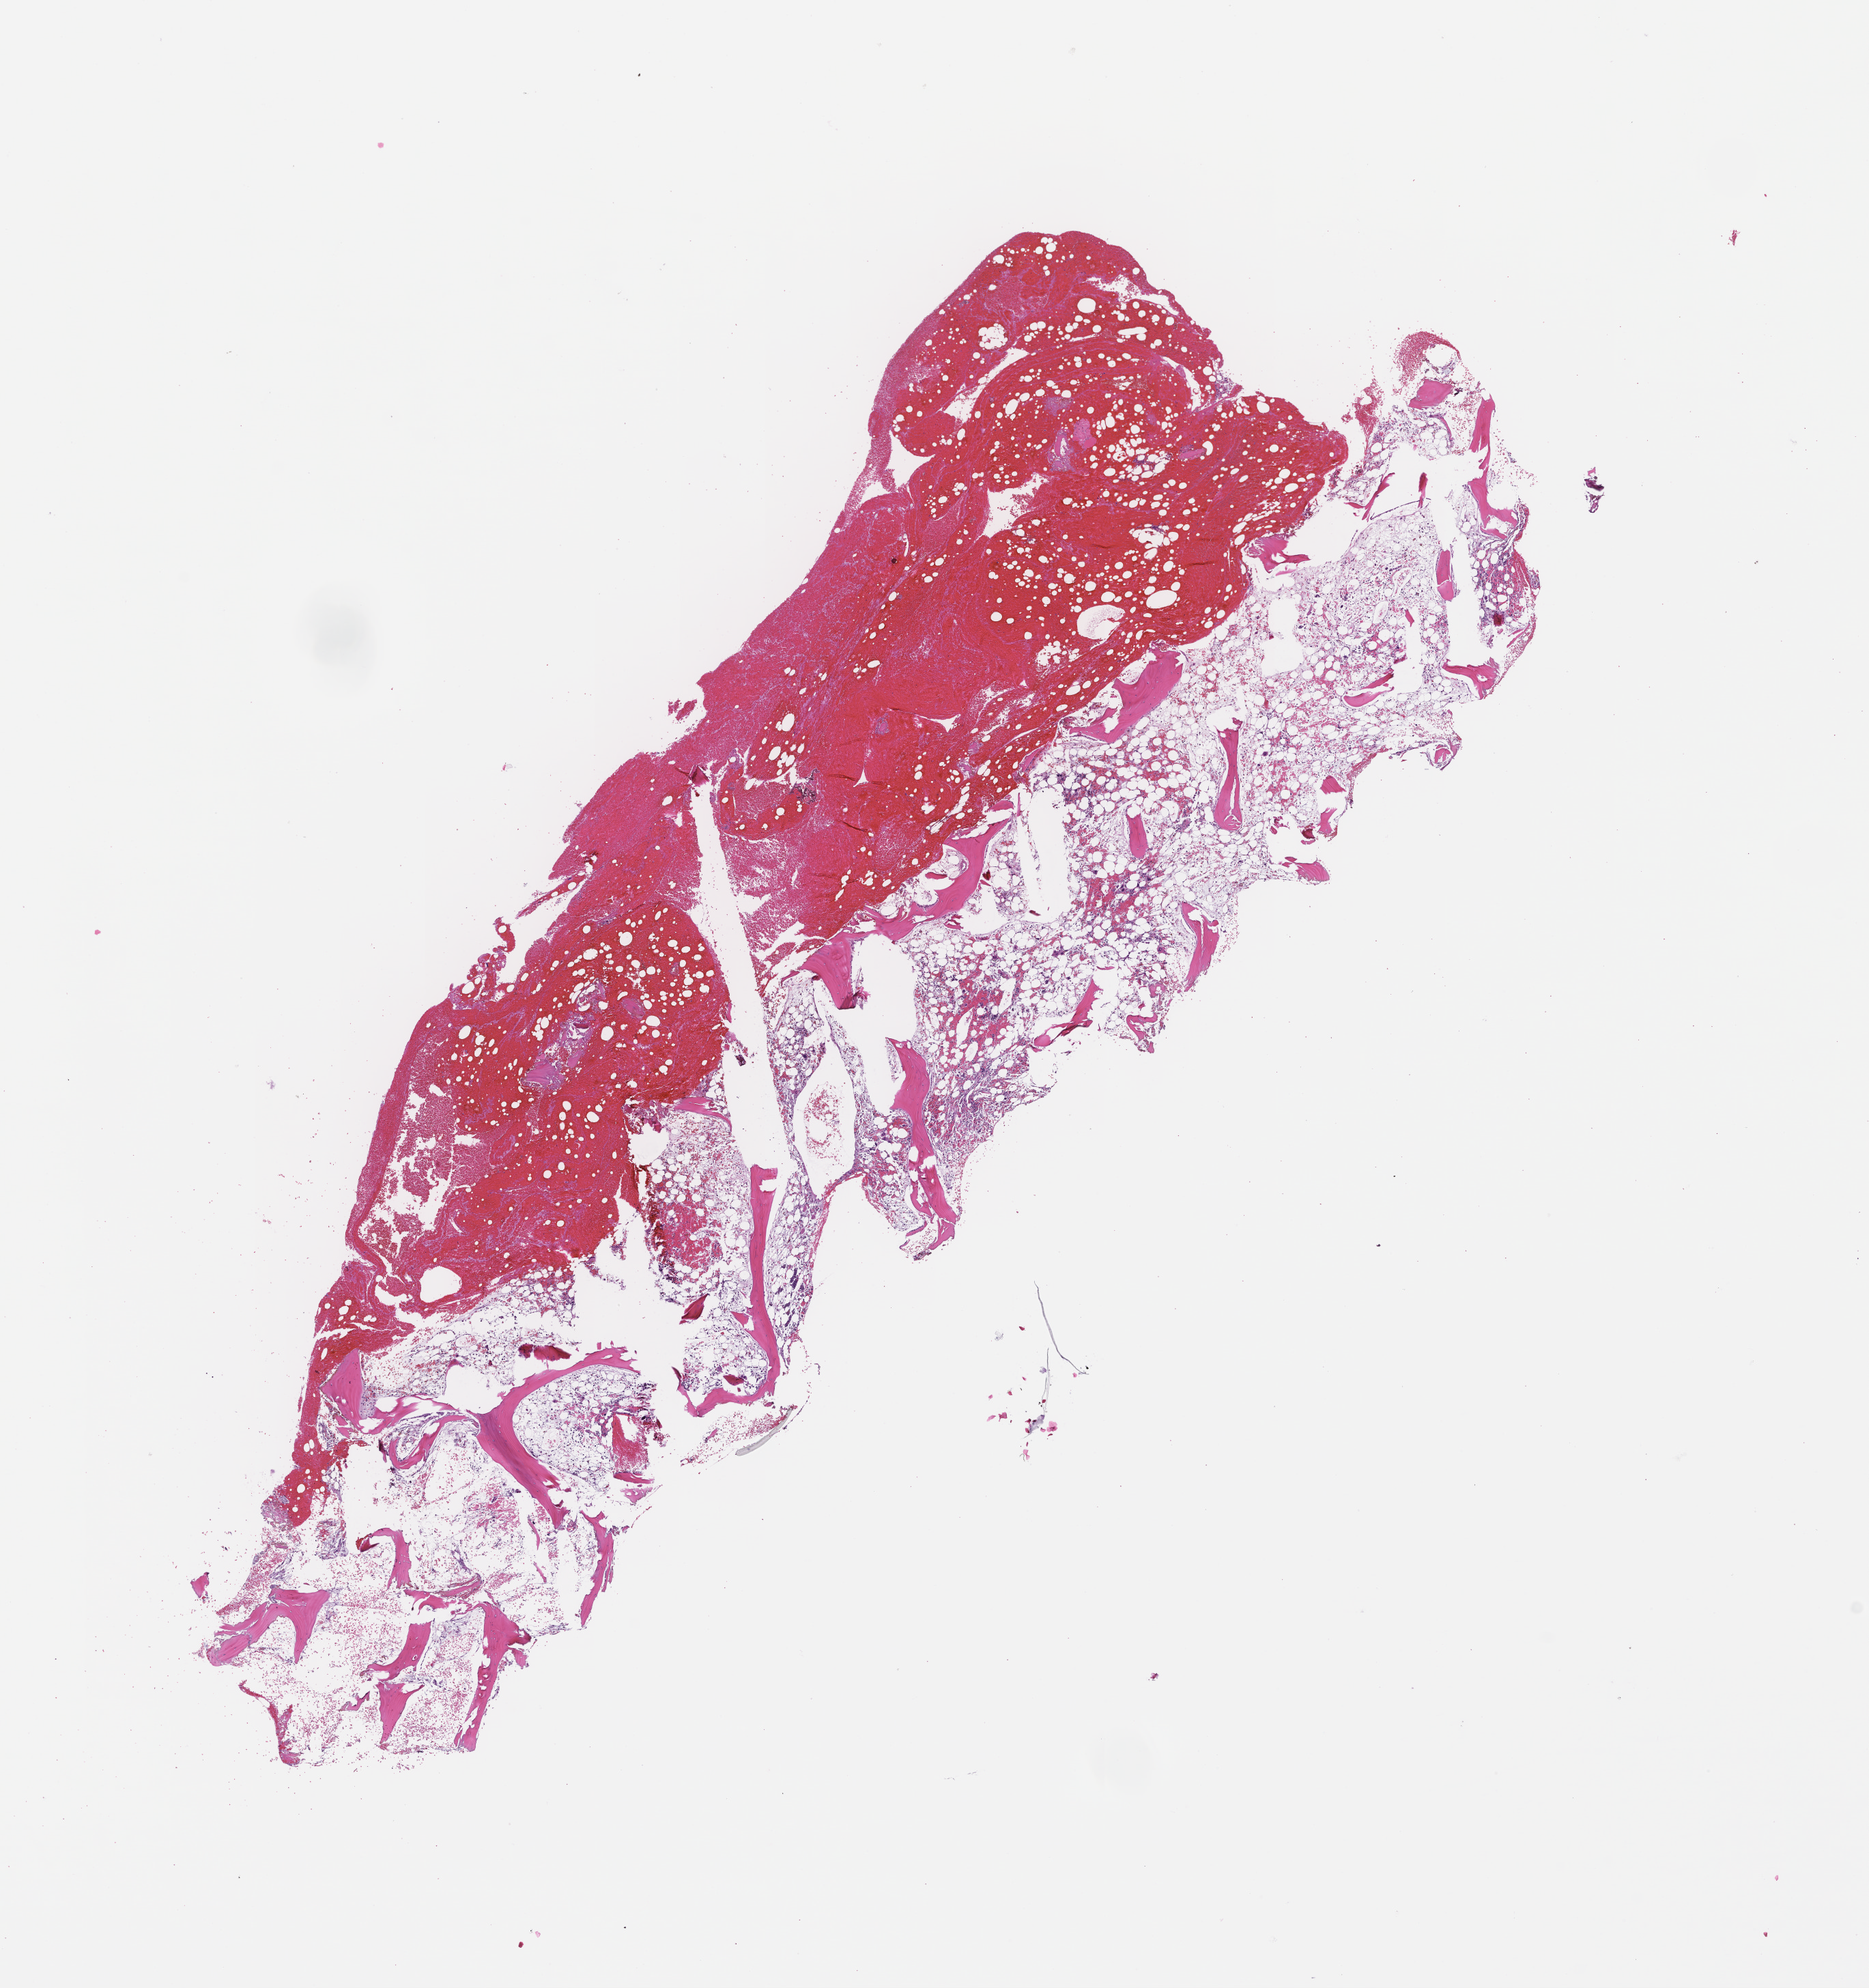
Digitized hematoxylin and eosin (H&E)-stained section — a low-resolution overview of the entire scanned area, about 11.1 x 11.8 mm, formalin-fixed paraffin-embedded section, tissue site: bone marrow, collected on treatment. Female patient.
- this section: primary tumour tissue
- diagnosis: Acute Myeloid Leukemia Not Otherwise Specified